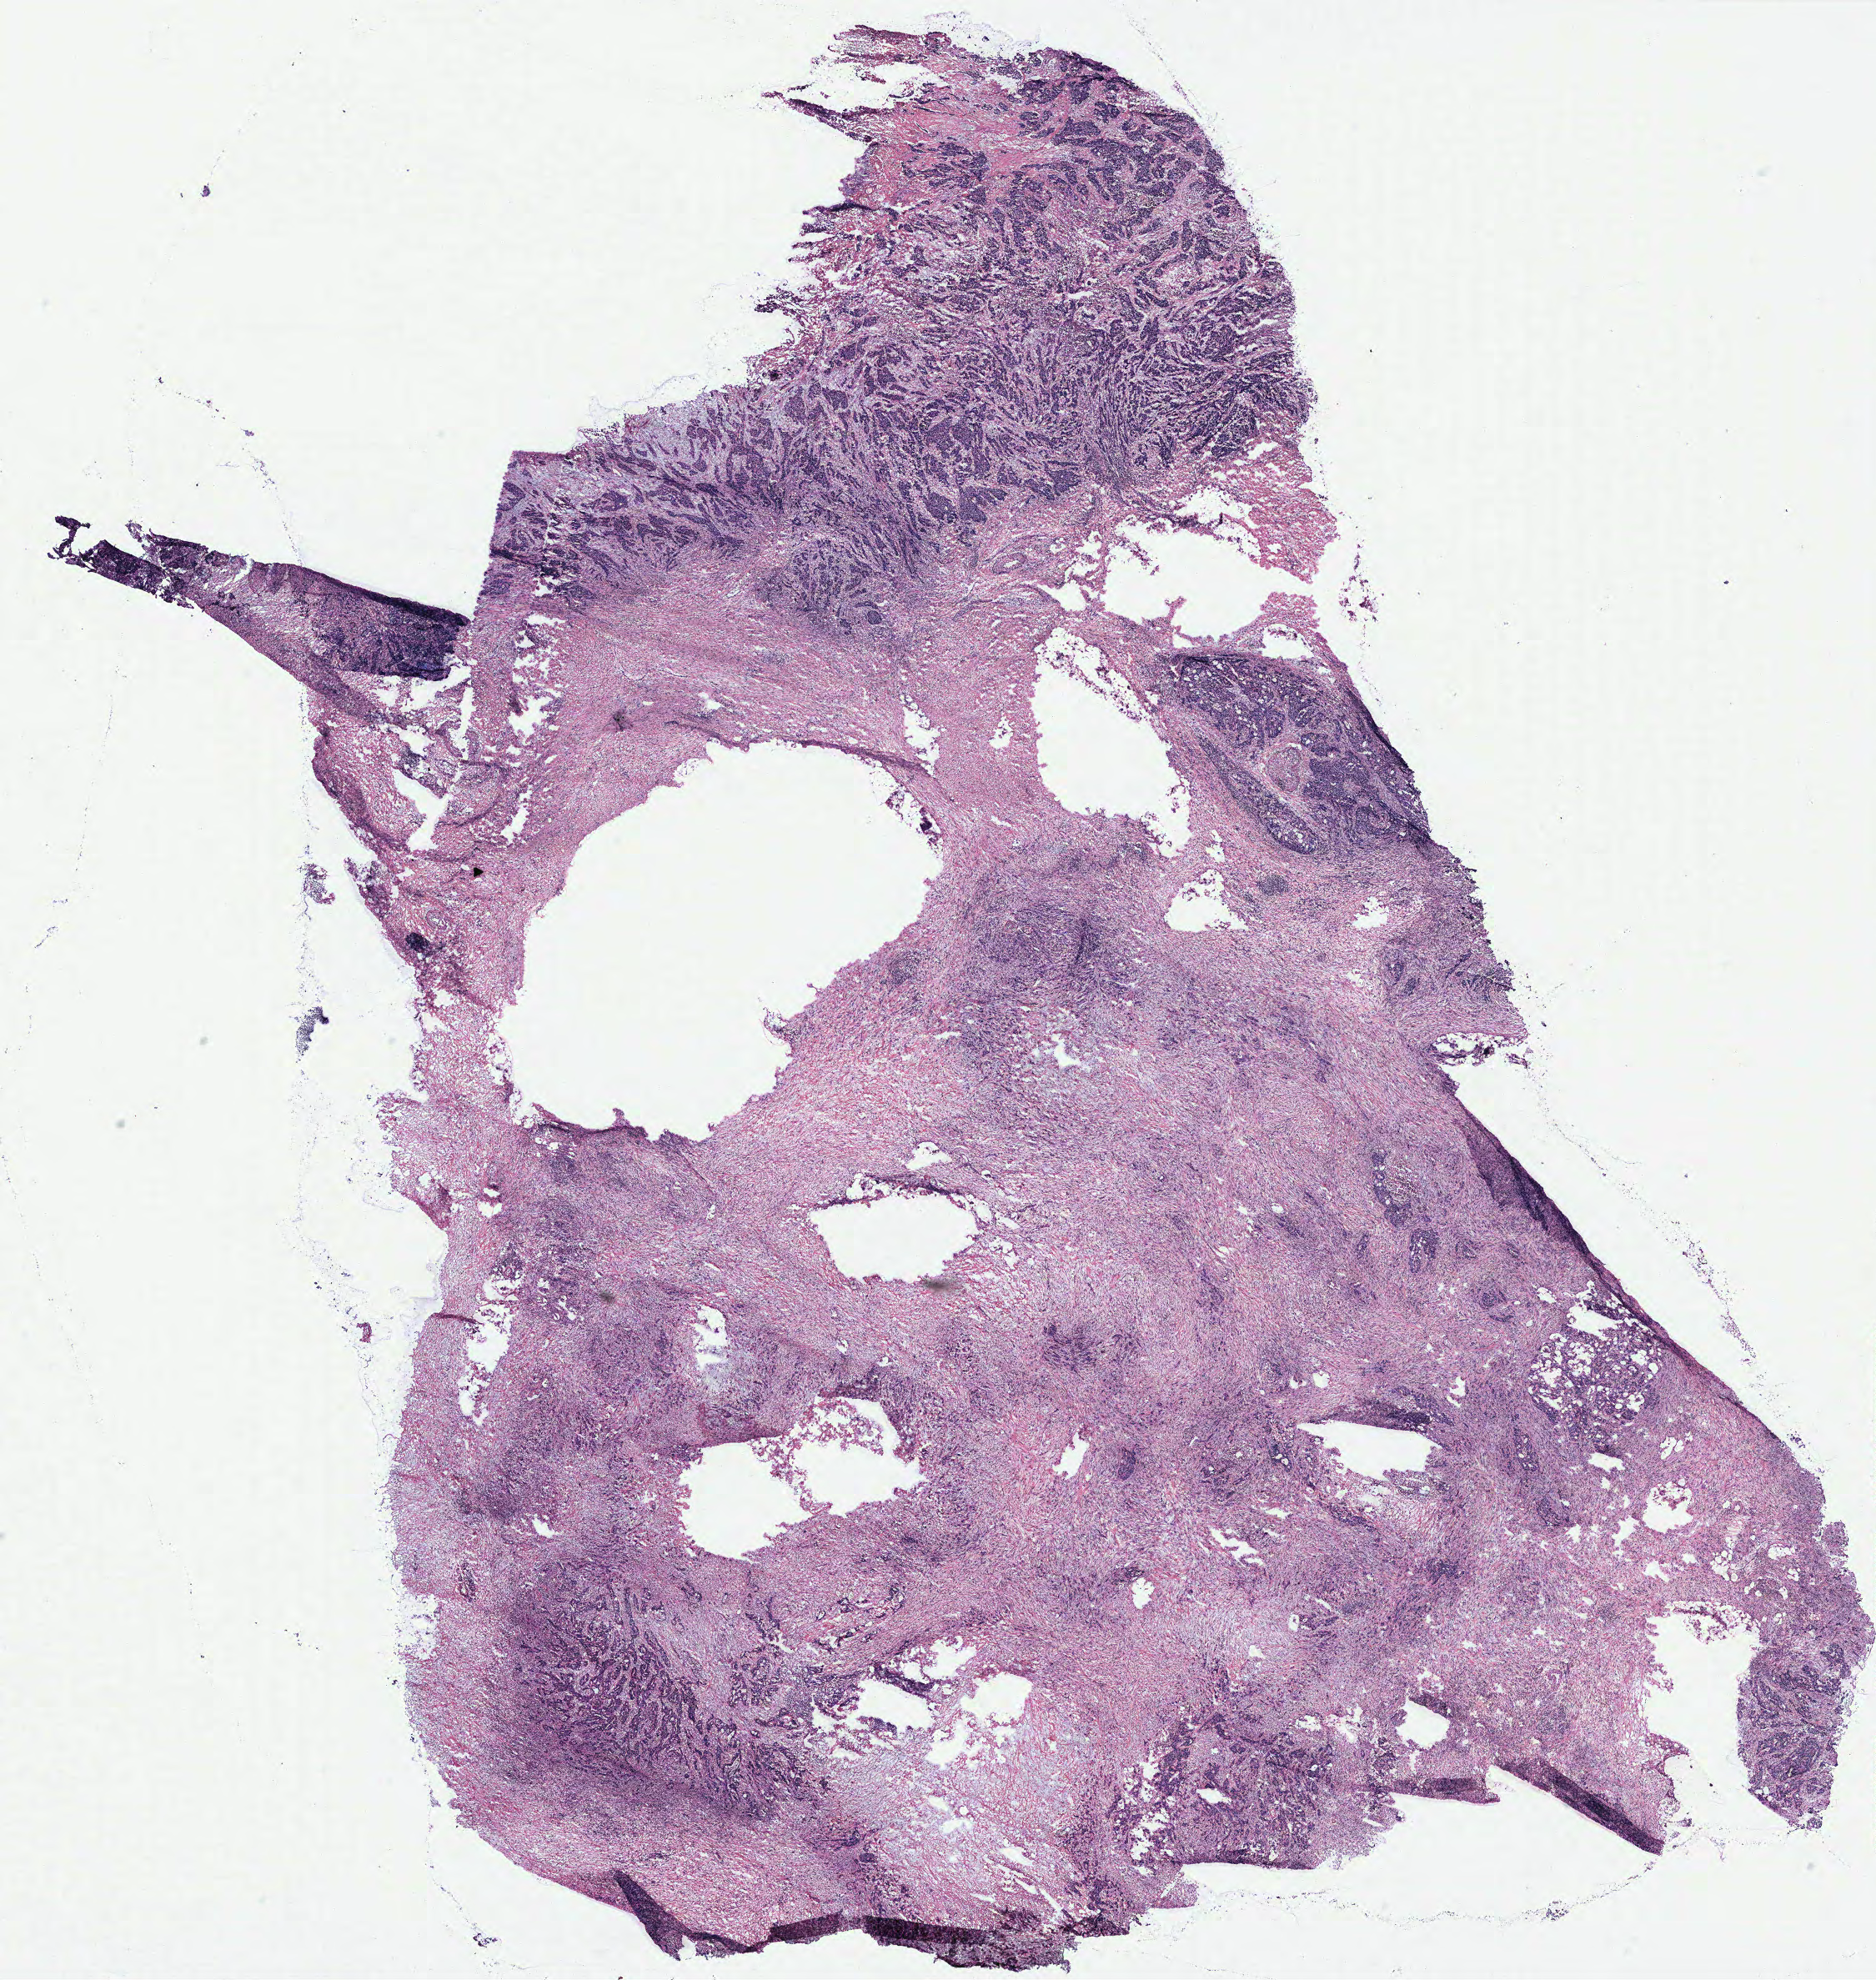
Whole-slide histology image, H&E-stained, whole scanned area (about 18.0 x 19.0 mm) shown as a low-resolution overview; colon, tissue type not recorded.
* patient diagnosis (cohort enrolment): colon cancer (colon)